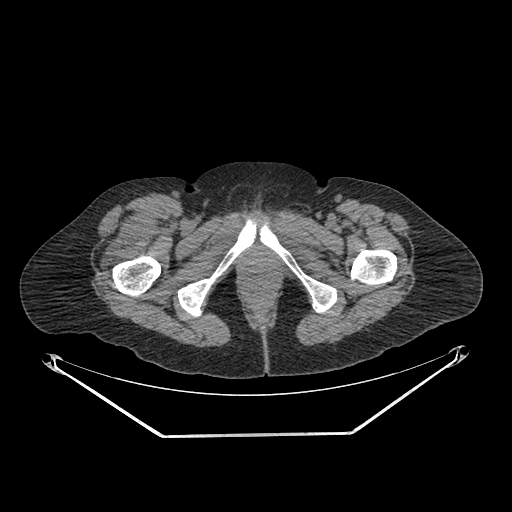
CT of an extremity soft-tissue mass (from a PET/CT study), one axial slice; slice 283 of 311 in the series (ordered by position); reconstruction kernel SOFT; soft-tissue window (W 400 / L 40 HU); 512 × 512 image matrix, field of view 500 × 500 mm. Female patient. From the clinical record (not read from this slice): histological type: pleiomorphic undifferentiated sarcoma; grade: high; site of the primary tumour: right quadricep.
Annotated regions visible in this slice (expert contour drawn on MRI and transferred to this co-registered scan by the dataset authors):
- tumour plus oedema (research contour): bounding box (x1, y1, x2, y2) in pixels: (103, 210, 165, 273)